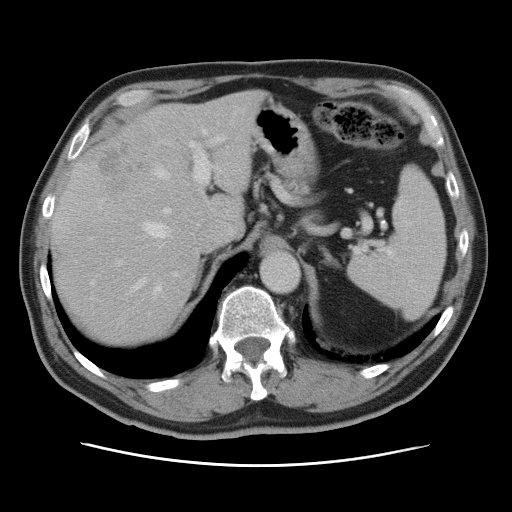
Contrast-enhanced abdominal CT, one axial slice; 120 kVp; intravenous contrast given; soft-tissue window (W 400 / L 40 HU); 512 × 512 image matrix. Male patient, age 69 years. From the clinical record (not read from this slice): diagnosis: colorectal cancer liver metastases, imaged before liver resection; multiple liver metastases: no; largest metastasis: 5 cm.
Outlined on this slice (expert manual segmentation):
- hepatic veins: bounding box [x1, y1, x2, y2] px = [133, 127, 208, 295]
- liver: [52, 91, 261, 348]
- planned liver remnant (the part of the liver to remain after resection): [51, 91, 261, 348]
- portal vein (with intrahepatic branches): [115, 120, 233, 276]
- liver metastasis: [98, 142, 143, 194]